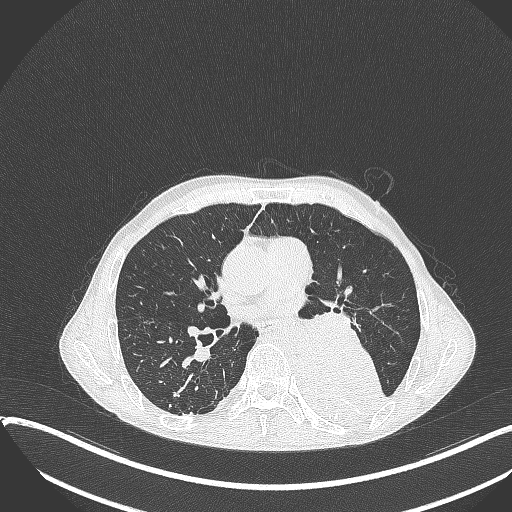
Chest CT, one axial slice; position 196 of 401 along the scan axis; reconstruction kernel B70f; 120 kVp; lung window (W 1500 / L -600 HU); 1 mm slice thickness; 512 × 512 image matrix. Patient: male, 57 years. Case-level facts recorded for this patient, not image findings: clinical TNM (as recorded): T4 N0 M0.
Structures marked on this image (rectangle marked by the reading radiologist):
- lung tumour (recorded histology: squamous cell carcinoma): bounding box [x1, y1, x2, y2] px = [287, 332, 386, 430]